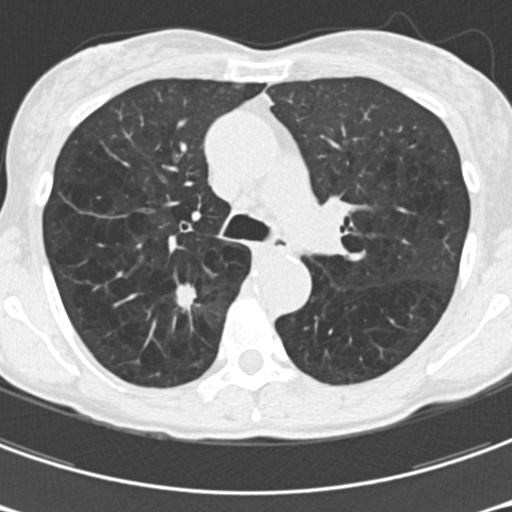
Low-dose screening chest CT, one axial slice. Slice 114 of 176 in the series (ordered by position). 120 kVp. Lung window (W 1500 / L -600 HU). 512 × 512 image matrix, field of view 277 × 277 mm.
Structures marked on this image (expert manual segmentation):
- lesion 1 (tumor, upper lobe of right lung): box from (x=176, y=284) to (x=199, y=311) px